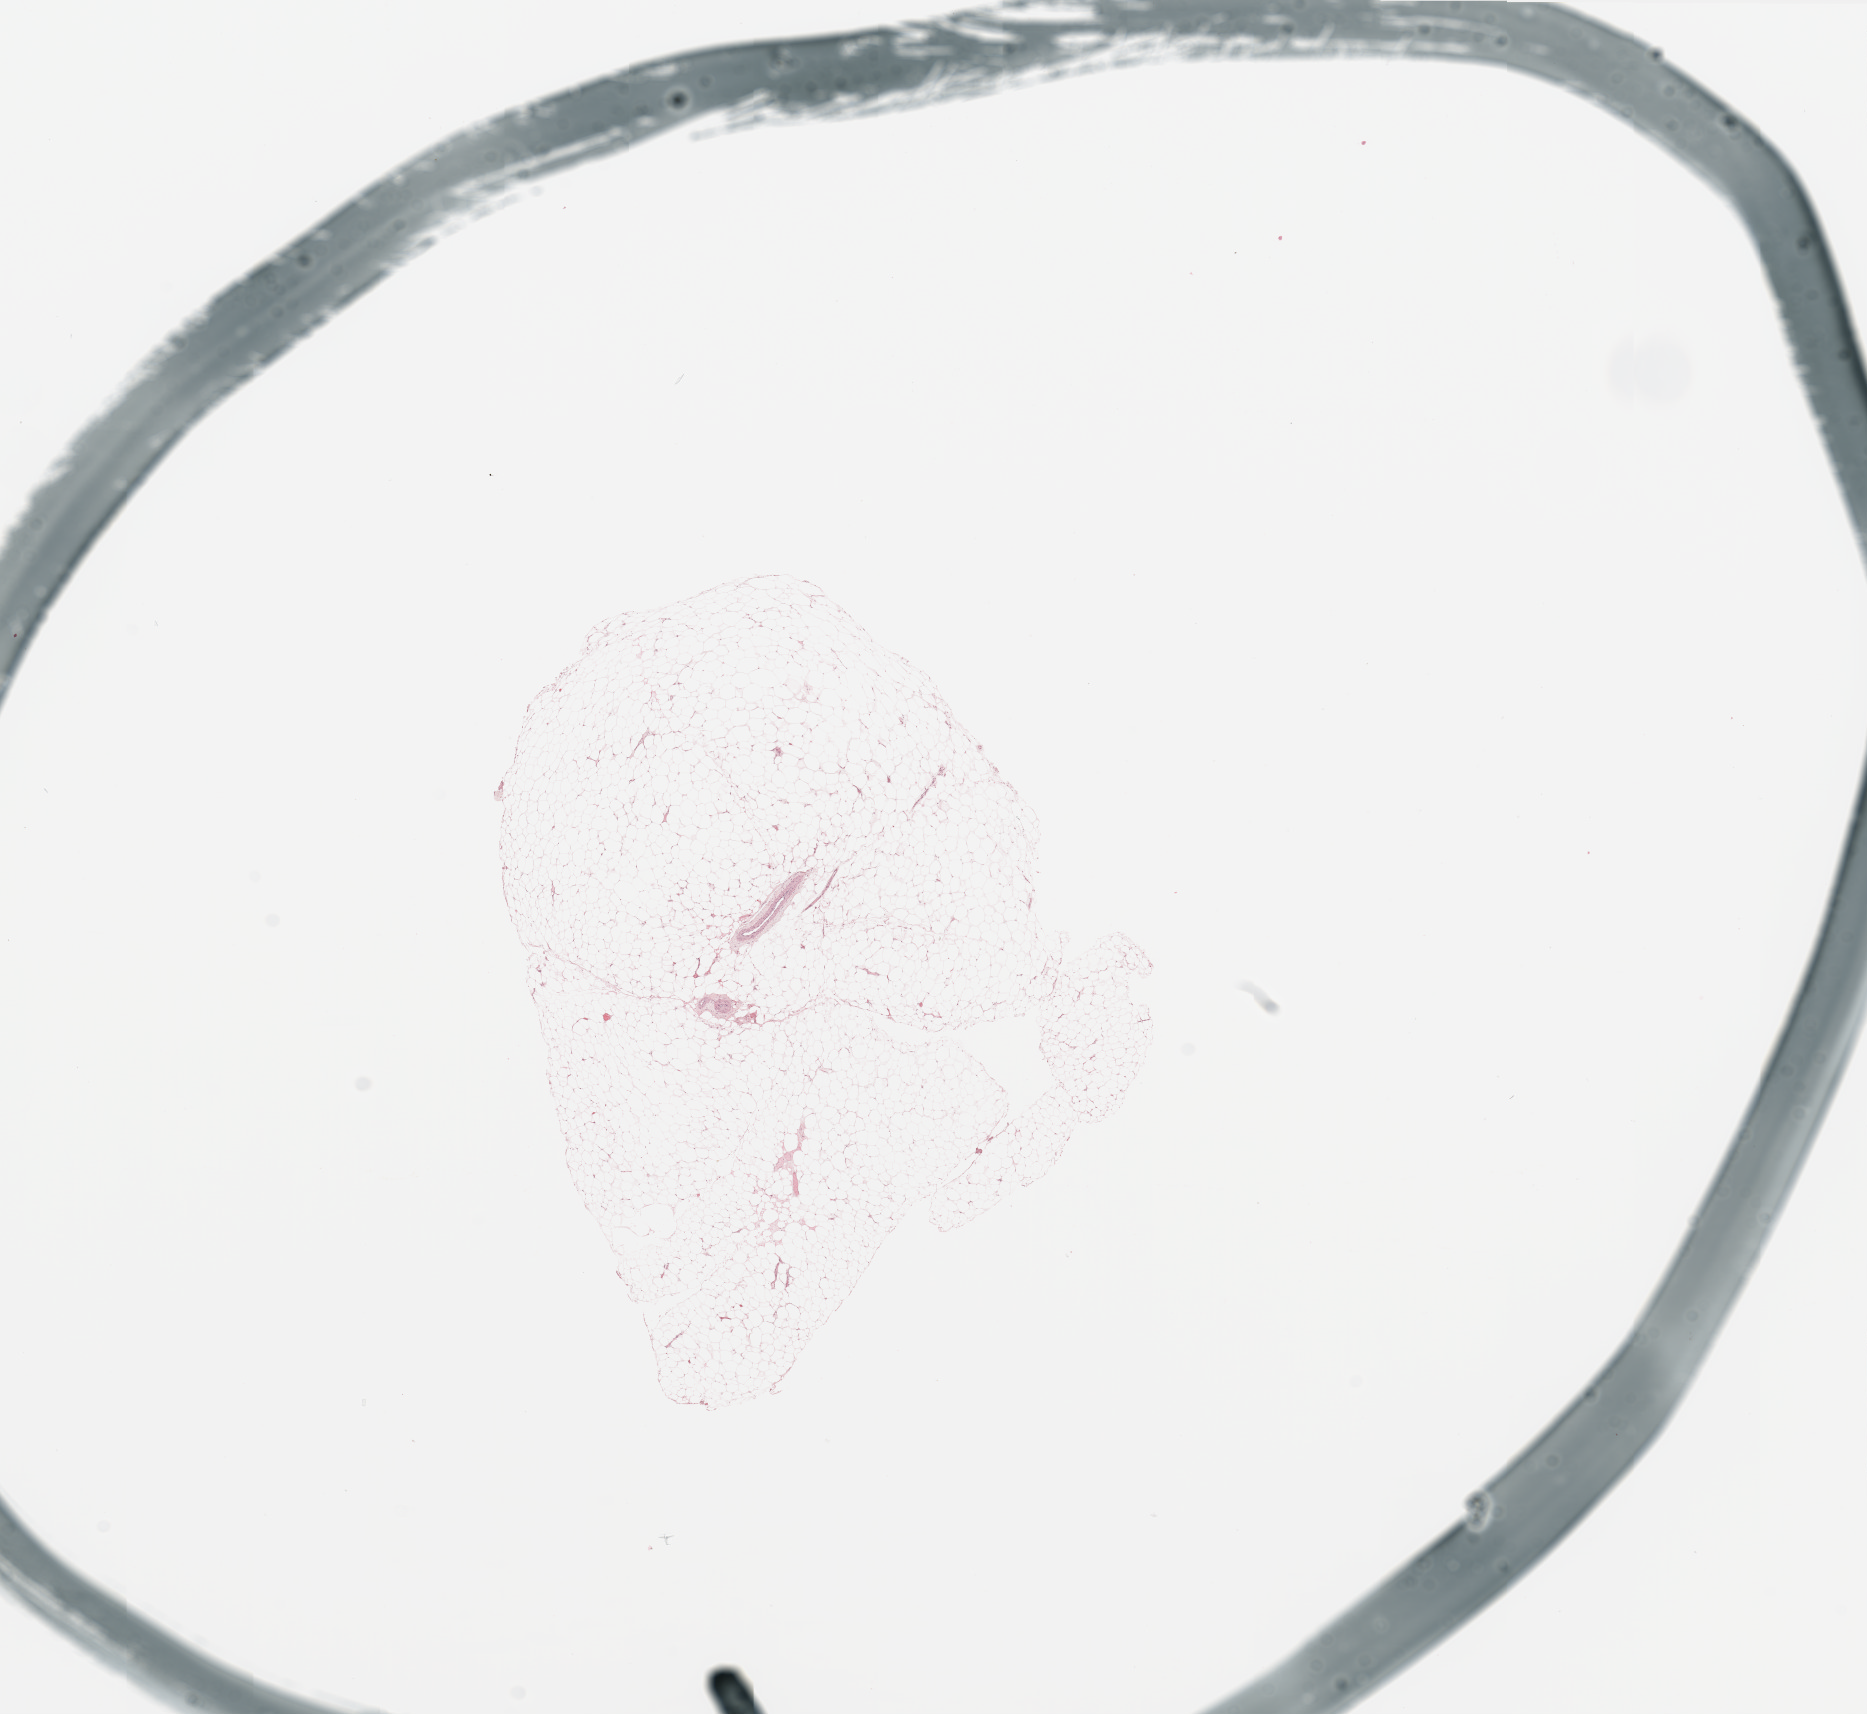
Whole-slide histology image, H&E, whole scanned area (about 14.8 x 13.6 mm, acquisition: 20x scan) shown as a low-resolution overview; kidney, normal (non-tumour) tissue. 68-year-old male patient.
This section: normal (non-tumour) tissue from the same patient. Patient diagnosis: Renal cell carcinoma, NOS.